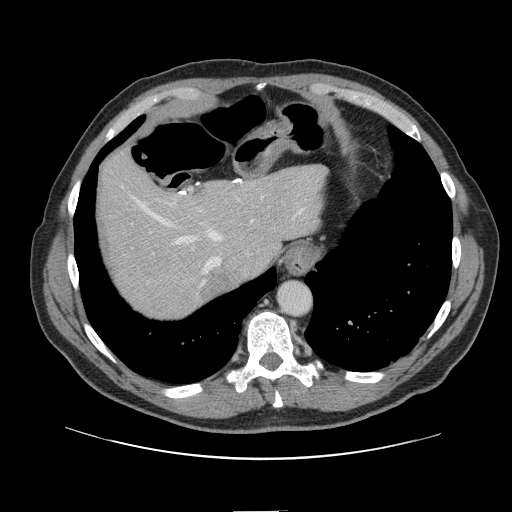
Contrast-enhanced abdominal CT, one axial slice; slice 118 of 161 in the series (ordered by position); 120 kVp; intravenous contrast given; soft-tissue window (W 400 / L 40 HU); 512 × 512 image matrix, field of view 412 × 412 mm. Male patient, age 66 years. From the clinical record (not read from this slice): diagnosis: colorectal cancer liver metastases, imaged before liver resection.
Outlined on this slice (expert manual segmentation):
- hepatic veins: box from (x=122, y=185) to (x=305, y=287) px
- liver: (x=99, y=153)–(x=323, y=317)
- planned liver remnant (the part of the liver to remain after resection): (x=99, y=154)–(x=322, y=301)
- portal vein (with intrahepatic branches): (x=170, y=192)–(x=188, y=206)
- liver metastasis: (x=202, y=270)–(x=230, y=299)